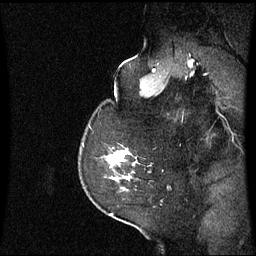
Breast MRI (dynamic contrast-enhanced), one sagittal slice. Position 48 of 60 along the scan axis. Dynamic contrast-enhanced series, image 2 of 3 at this slice position (ordered by acquisition). 1.5 T. TE 4.2 ms, TR 8.9 ms. 256 × 256 image matrix. Female patient, age 58 years. From the clinical record (not read from this slice): setting: breast cancer imaged before/during neoadjuvant chemotherapy; receptor status: triple-negative.
Structures marked on this image (semi-automatic segmentation, software-assisted and operator-edited):
- analysis volume of interest (the breast-tissue region the enhancement analysis was run in; not a lesion): box from (x=110, y=148) to (x=137, y=191) px
- tumour enhancement mask (voxels above the 70 % enhancement threshold inside the analysis volume of interest): (x=112, y=152)–(x=127, y=181)